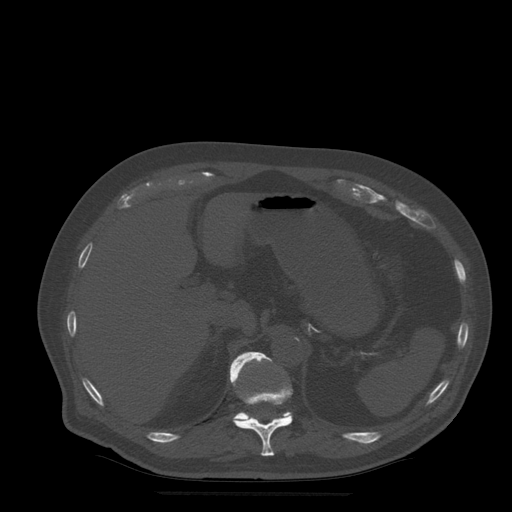
CT including the spine, one axial slice; position 237 of 522 along the scan axis; bone window (W 1800 / L 400 HU); 1.25 mm slice thickness; 512 × 512 image matrix. Patient age 72 years. From the clinical record (not read from this slice): primary cancer: prostate.
Structures marked on this image (semi-automatic segmentation, software-assisted and operator-edited):
- T11 vertebra: bounding box (x1, y1, x2, y2) in pixels: (233, 385, 293, 457)
- T12 vertebra: (230, 352, 291, 420)